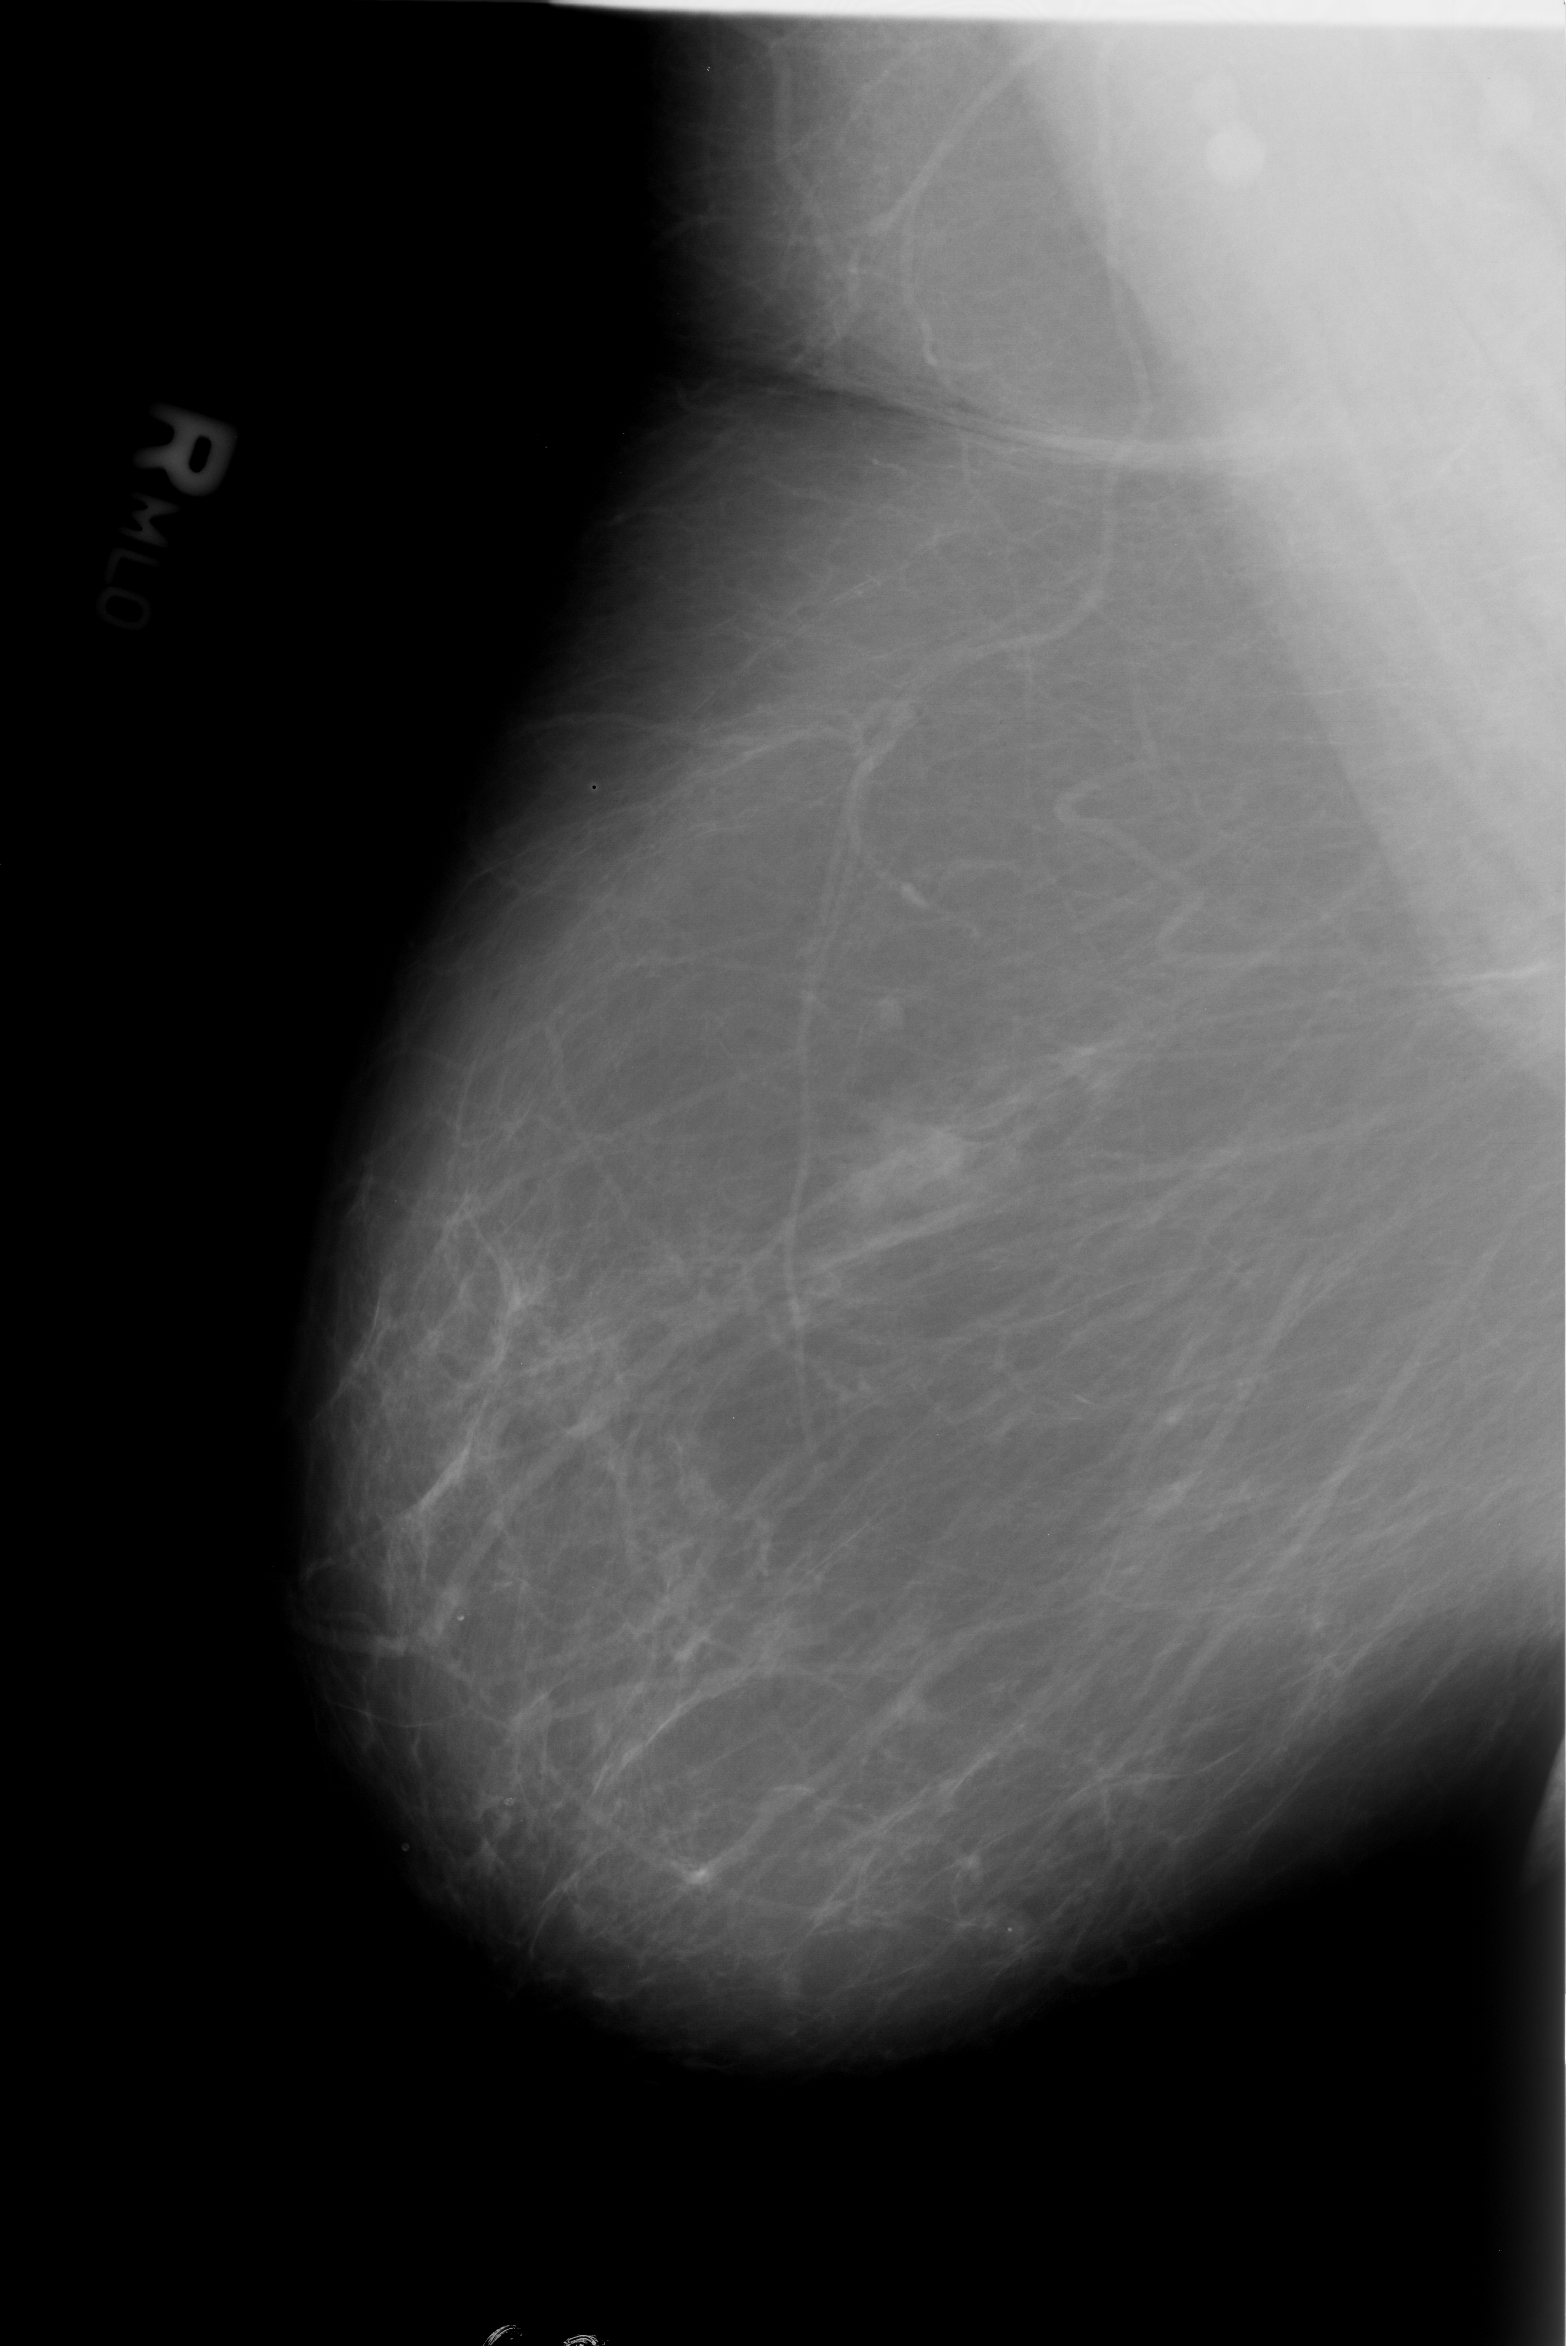
Digitized screen-film mammogram; right breast; mediolateral oblique (MLO) view; breast composition: almost entirely fatty (BI-RADS density category 1 of 4); 1568 × 2346 image matrix.
Expert-marked regions of interest on this film, with their recorded descriptors:
- mass, shape lobulated / irregular, margins microlobulated / ill defined; BI-RADS assessment category 4; pathology (as recorded): benign: bounding box (x1, y1, x2, y2) in pixels: (843, 1112, 960, 1208)